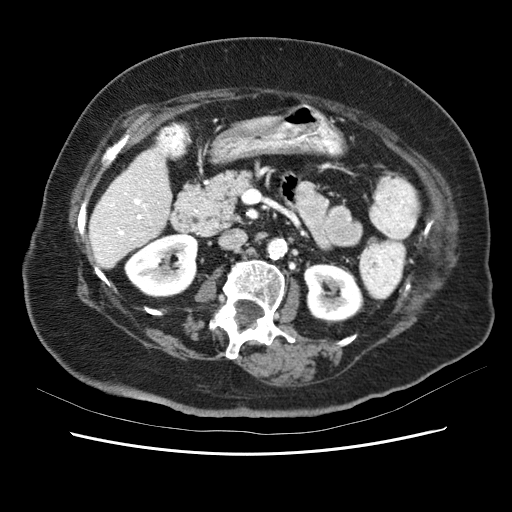
Contrast-enhanced abdominal CT (liver protocol), one axial slice. Slice 18 of 62 in the series (ordered by position). Reconstruction kernel STANDARD. Soft-tissue window (W 400 / L 40 HU). 2.5 mm slice thickness. 512 × 512 image matrix, field of view 340 × 340 mm. From the clinical record (not read from this slice): diagnosis: hepatocellular carcinoma (patient treated with transarterial chemoembolisation; whether this scan precedes or follows treatment is not stated here); TNM stage (as recorded): Stage-I.
Annotated regions visible in this slice (semi-automatic segmentation, software-assisted and operator-edited):
- liver parenchyma outside the tumour (the mass and vessels are separate outlines, so this box may not span the whole liver): bounding box [x1, y1, x2, y2] px = [88, 140, 172, 272]
- liver vessels: [94, 142, 170, 267]